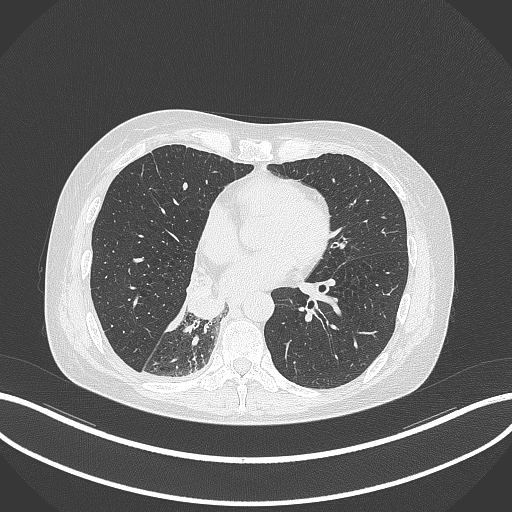
Chest CT, one axial slice. Slice 125 of 329 in the series (ordered by position). 120 kVp. Lung window (W 1500 / L -600 HU). 1 mm slice thickness. 512 × 512 image matrix. Patient: female, 63 years. From the clinical record (not read from this slice): clinical TNM (as recorded): T1c N0 M0.
Structures marked on this image (rectangle marked by the reading radiologist):
- lung tumour (recorded histology: adenocarcinoma): bounding box [x1, y1, x2, y2] px = [183, 267, 229, 321]